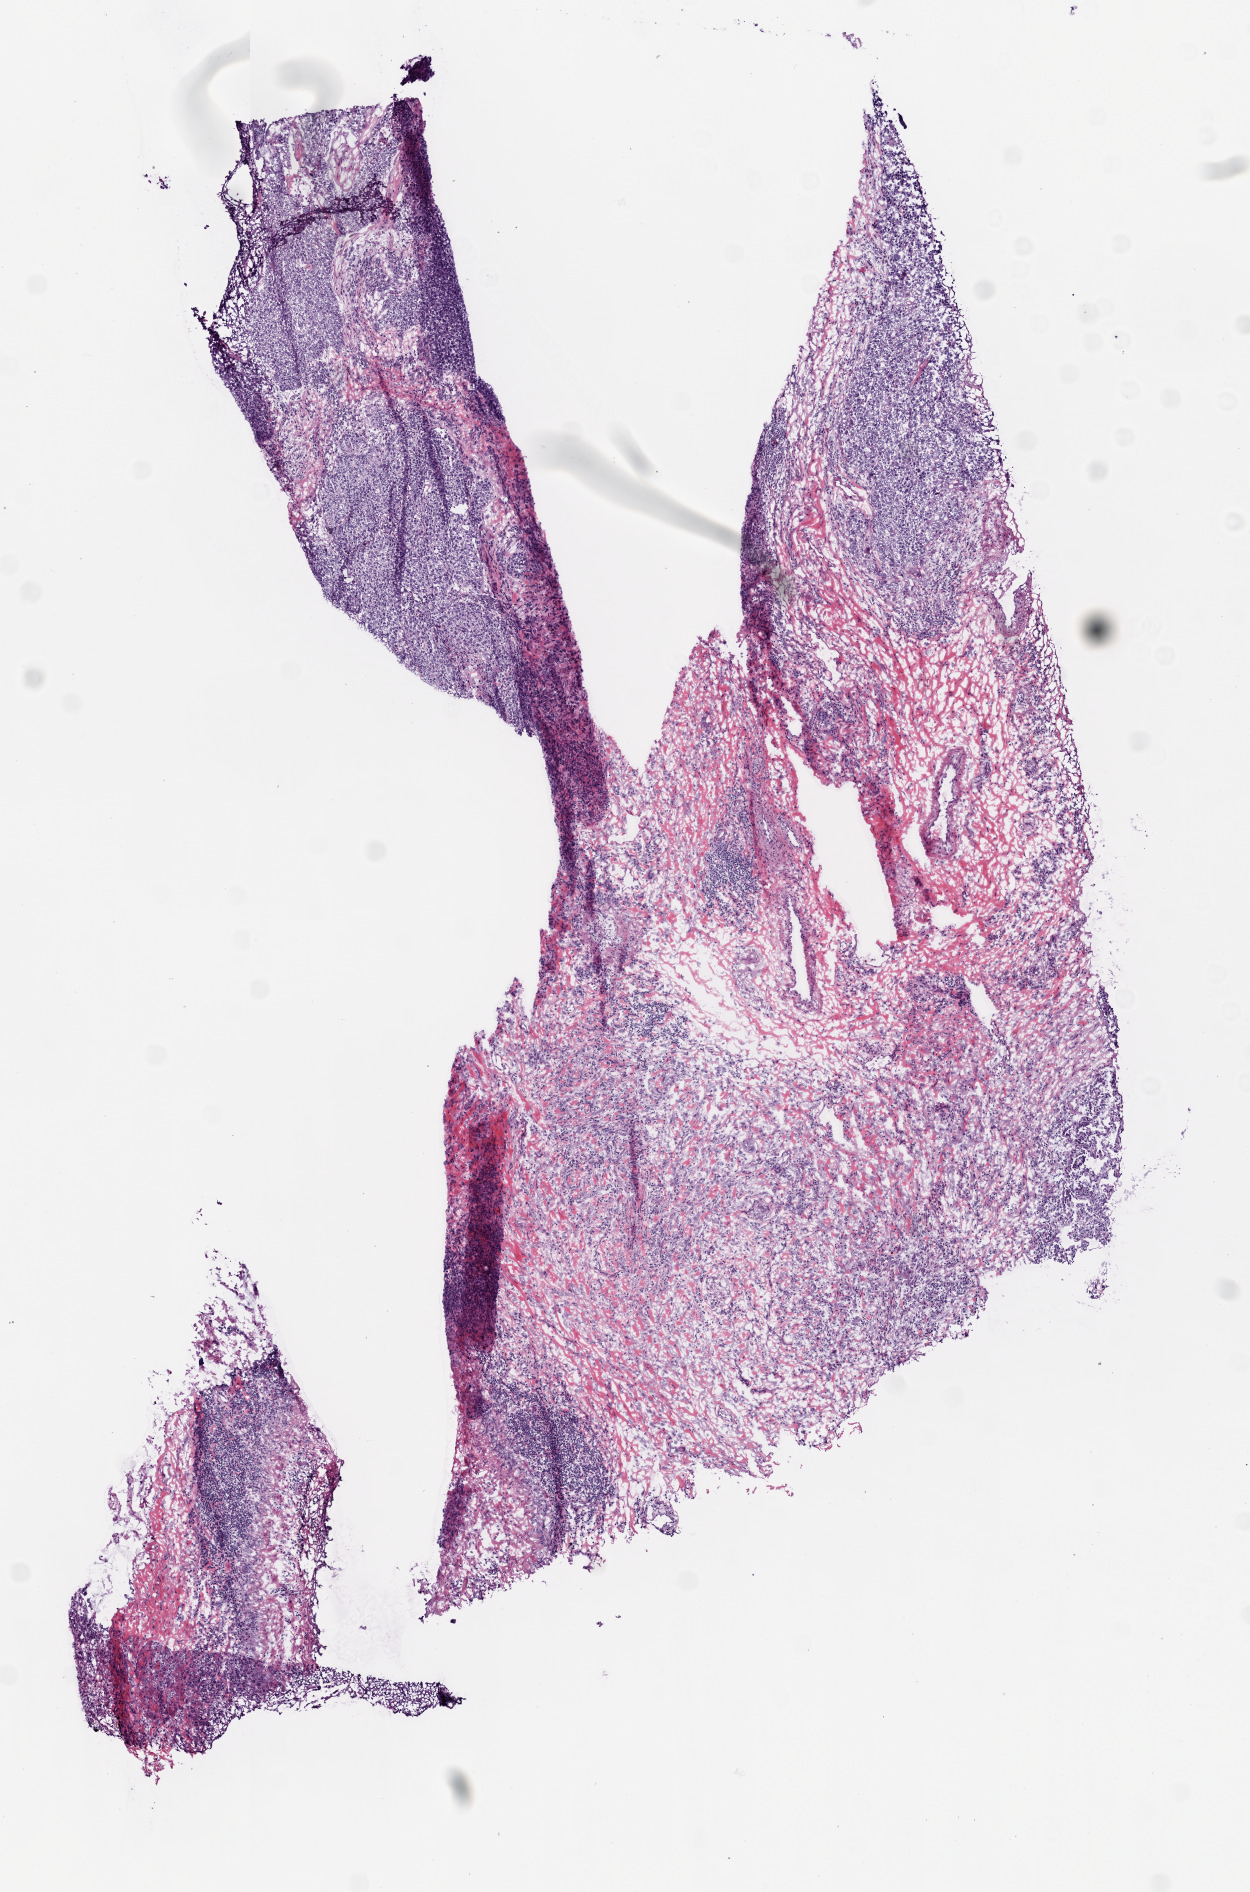
Whole-slide histology image, H&E — shown as a low-resolution overview of the whole scanned area (about 5.0 x 7.6 mm, from a 20x scan); frozen section; primary tumour sample from the lung. Male, age 68 years at initial diagnosis. Pathologist review of this section (percent, as recorded): tumour cells 45%, tumour nuclei 60%, normal cells 50%, stromal cells 5%, necrosis 0%.
AJCC pathologic stage: IIIB (6th edition). Laterality: right. Pathologic diagnosis: Squamous cell carcinoma, NOS (middle lobe, lung).